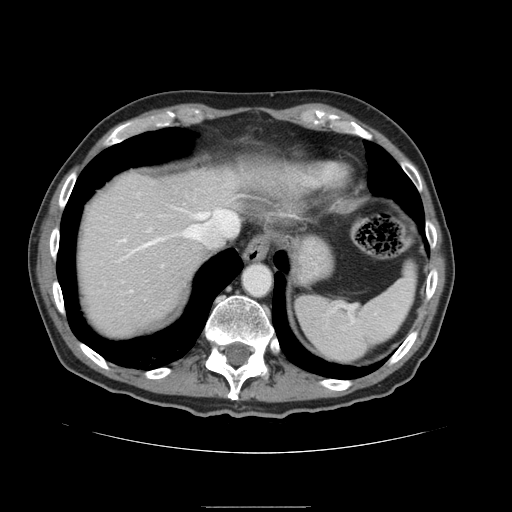
Contrast-enhanced abdominal CT, one axial slice; slice 128 of 168 in the series (ordered by position); intravenous contrast given; soft-tissue window (W 400 / L 40 HU); 512 × 512 image matrix, field of view 386 × 386 mm. Male patient, age 74 years. Case-level facts recorded for this patient, not image findings: diagnosis: colorectal cancer liver metastases, imaged before liver resection; multiple liver metastases: no.
Annotated regions visible in this slice (expert manual segmentation):
- hepatic veins: bounding box <132,210,237,252> (left, top, right, bottom; pixels)
- liver: <76,165,244,339>
- planned liver remnant (the part of the liver to remain after resection): <77,165,243,339>